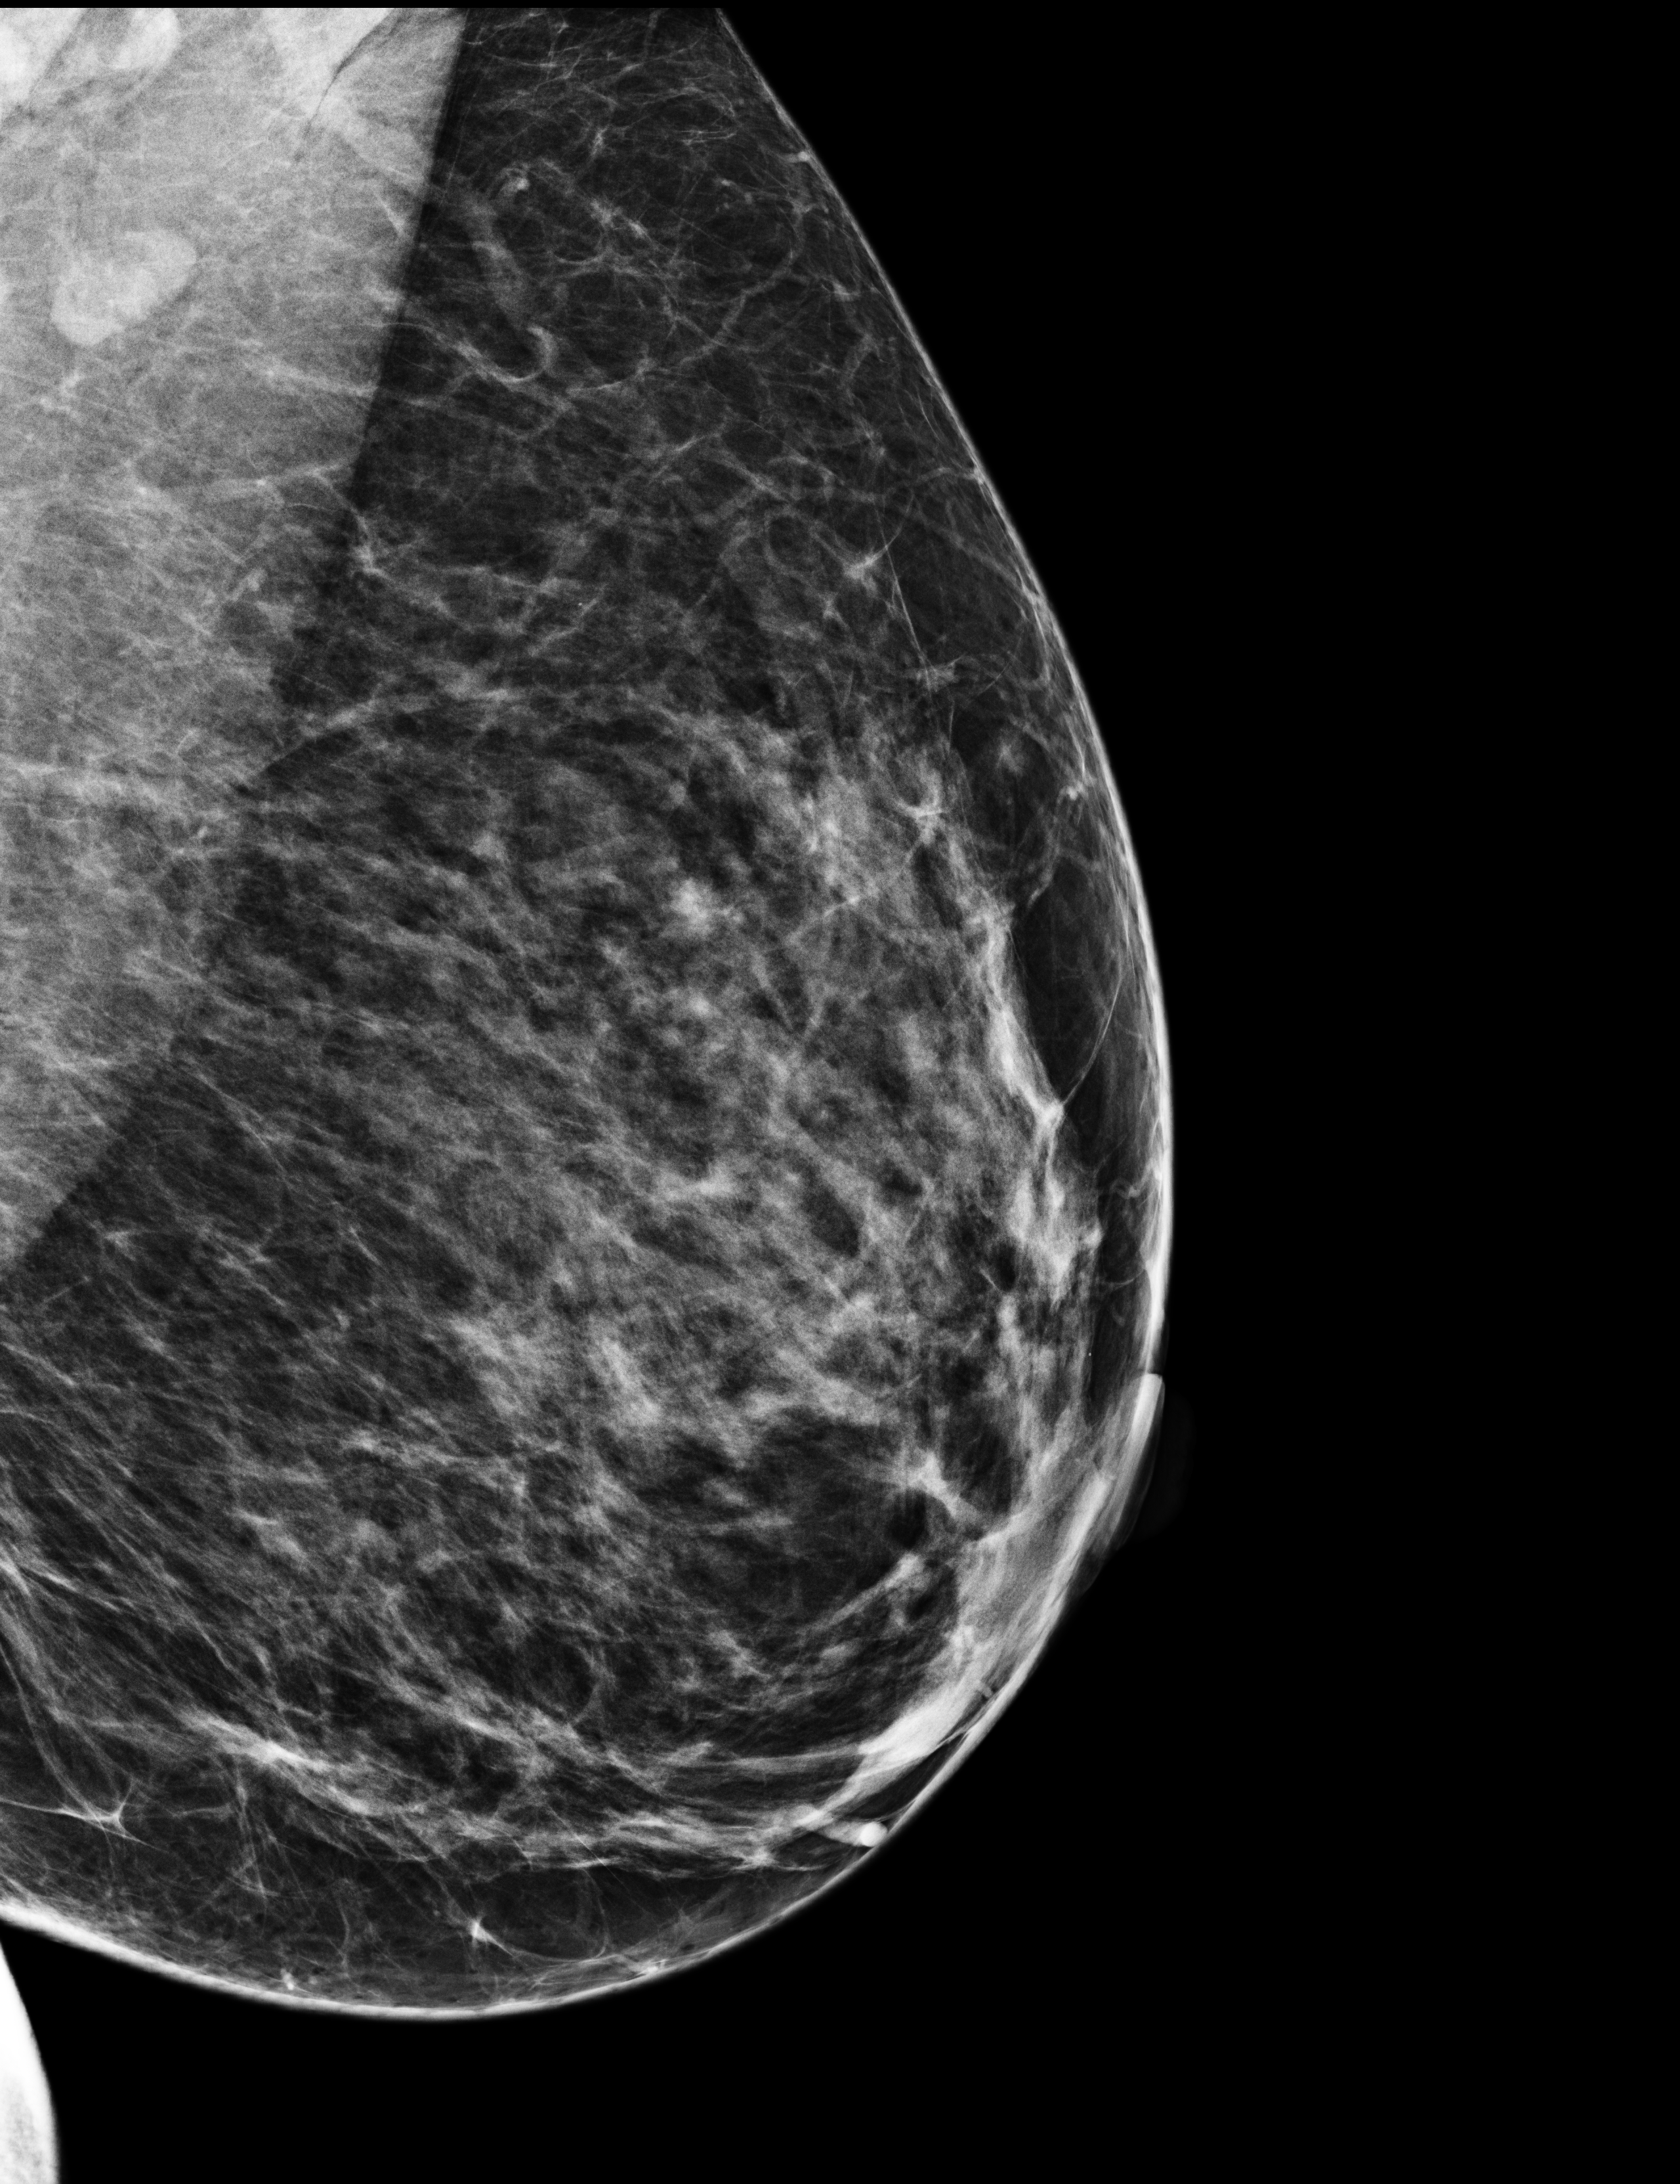
Digital mammogram (FFDM), left breast, MLO view, annual screening mammography examination, system: Selenia Dimensions. Female patient, age 43 years.
- breast density at the screening exam (both breasts): heterogeneously dense (BI-RADS density category c)
- final BI-RADS category for the screening round (tomosynthesis exam, both breasts): category 1
- recall: no recall after this screen